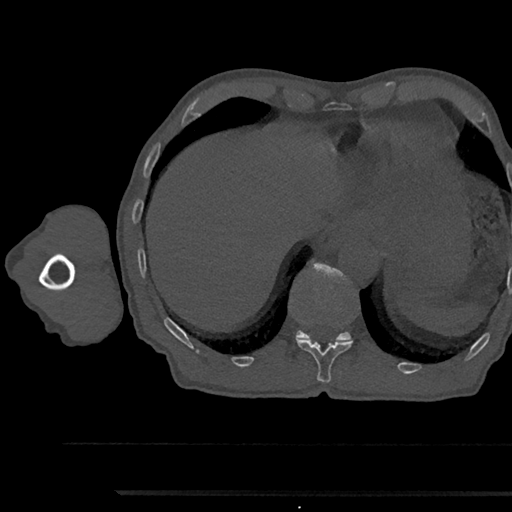
CT including the spine, one axial slice; position 760 of 797 along the scan axis; reconstruction kernel Br40s/3; bone window (W 1800 / L 400 HU); 0.5 mm slice thickness; 512 × 512 image matrix, field of view 367 × 367 mm. Patient: male, 79 years. From the clinical record (not read from this slice): primary cancer: prostate.
Annotated regions visible in this slice (semi-automatic segmentation, software-assisted and operator-edited):
- T11 vertebra: box from (x=296, y=338) to (x=352, y=383) px
- T12 vertebra: (x=296, y=264)–(x=352, y=342)